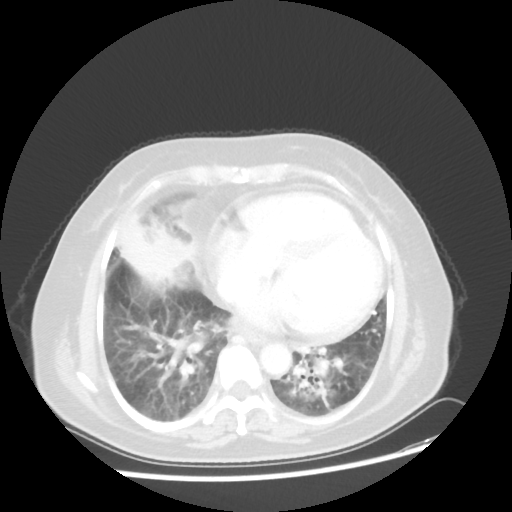
Chest CT, one axial slice. Slice 17 of 45 in the series (ordered by position). Reconstruction kernel STANDARD. 100 kVp. Lung window (W 1500 / L -600 HU). 512 × 512 image matrix, field of view 359 × 359 mm. Patient: female, 67 years. From the clinical record (not read from this slice): clinical TNM (as recorded): T2a N3 M1a.
Annotated regions visible in this slice (rectangle marked by the reading radiologist):
- lung tumour (recorded histology: adenocarcinoma): box from (x=121, y=206) to (x=187, y=291) px